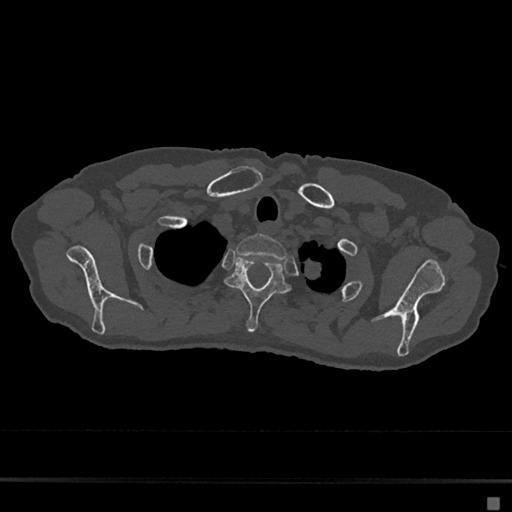
CT including the spine, one axial slice. Slice 579 of 797 in the series (ordered by position). Reconstruction kernel Br40s/3. Bone window (W 1800 / L 400 HU). 0.5 mm slice thickness. 512 × 512 image matrix, field of view 360 × 360 mm. Female patient, age 68 years. Case-level facts recorded for this patient, not image findings: primary cancer: renal.
Structures marked on this image (semi-automatically segmented with operator editing):
- T1 vertebra: box from (x=236, y=234) to (x=287, y=261) px
- T2 vertebra: (x=225, y=255)–(x=291, y=332)